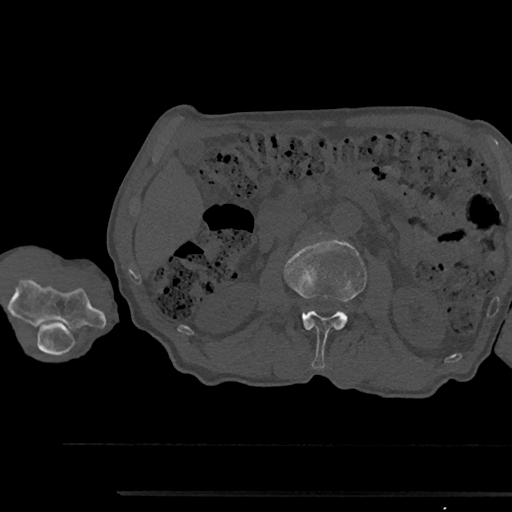
CT including the spine, one axial slice; slice 553 of 797 in the series (ordered by position); reconstruction kernel Br40s/3; bone window (W 1800 / L 400 HU); 0.5 mm slice thickness; 512 × 512 image matrix, field of view 367 × 367 mm. Male patient, age 79 years. From the clinical record (not read from this slice): primary cancer: prostate.
Outlined on this slice (semi-automatically segmented with operator editing):
- L2 vertebra: box from (x=284, y=239) to (x=367, y=369) px